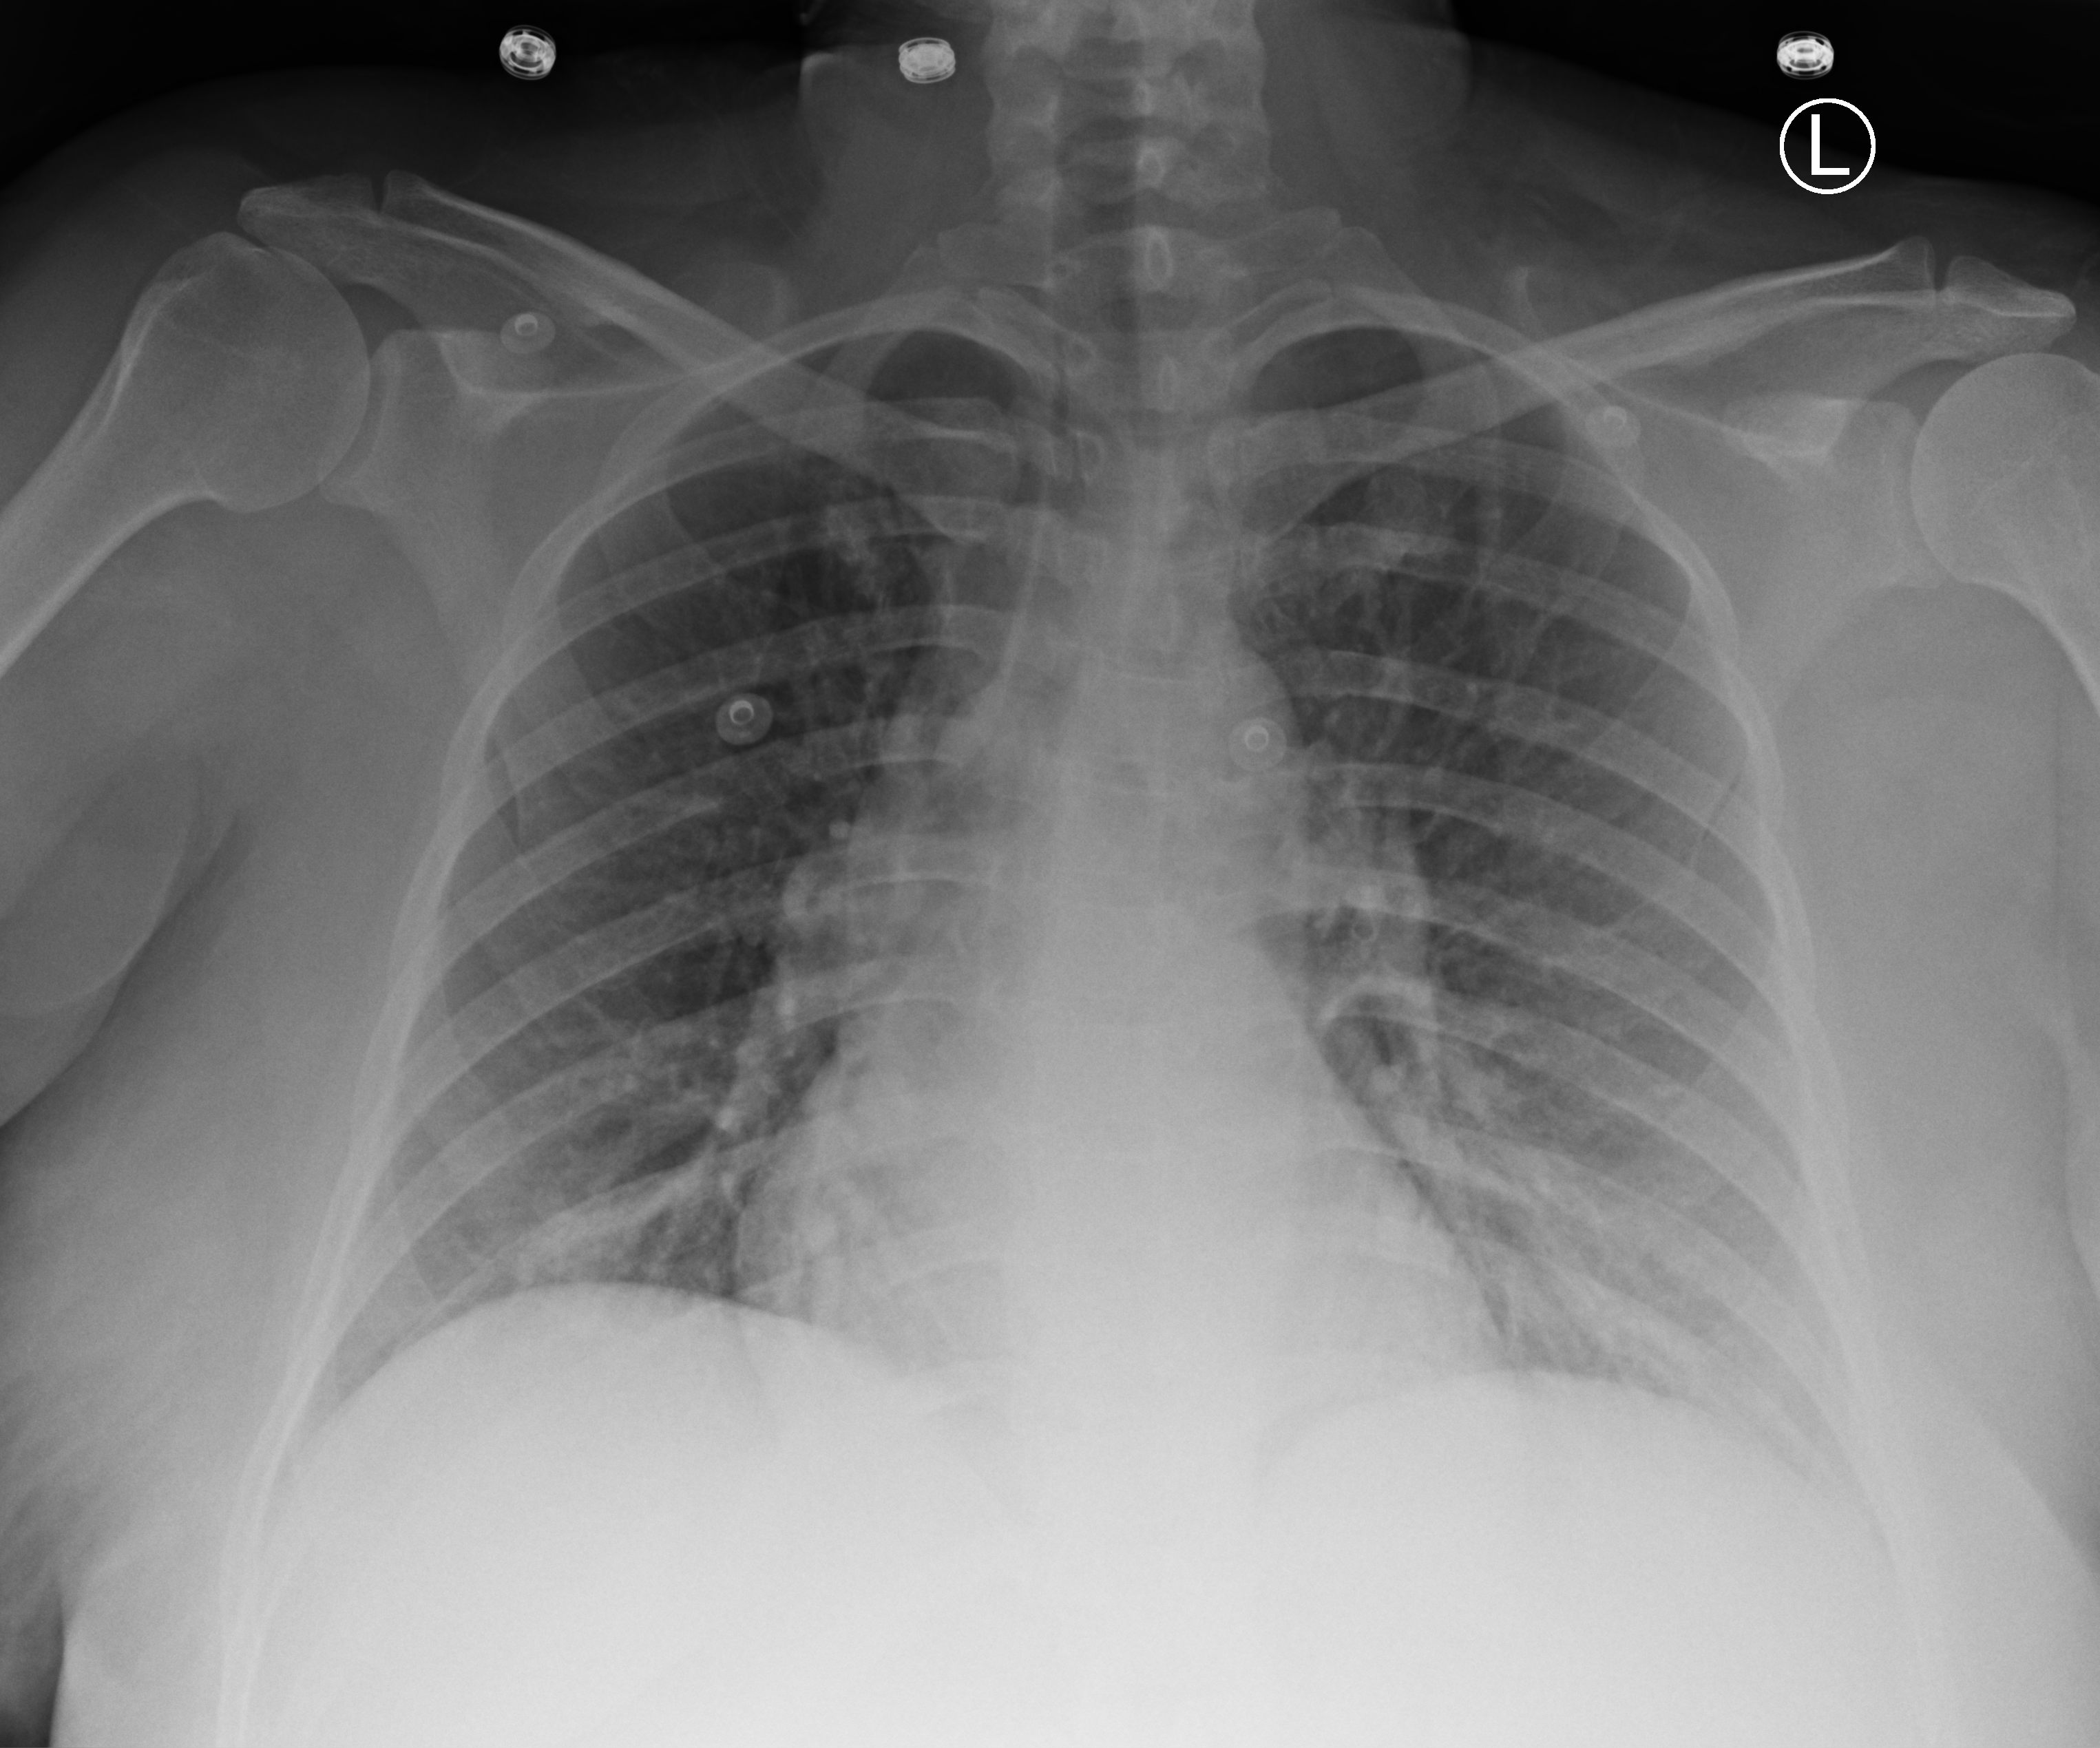
Chest X-ray (portable), anteroposterior (AP) projection. Female patient hospitalised with COVID-19, age 18–59 years.
From the hospital-stay record, not from the radiograph (when in the stay this image was taken is not recorded):
- length of hospital stay: 3 days
- mechanically ventilated during this hospital stay: no
- admitted to intensive care during this hospital stay: no